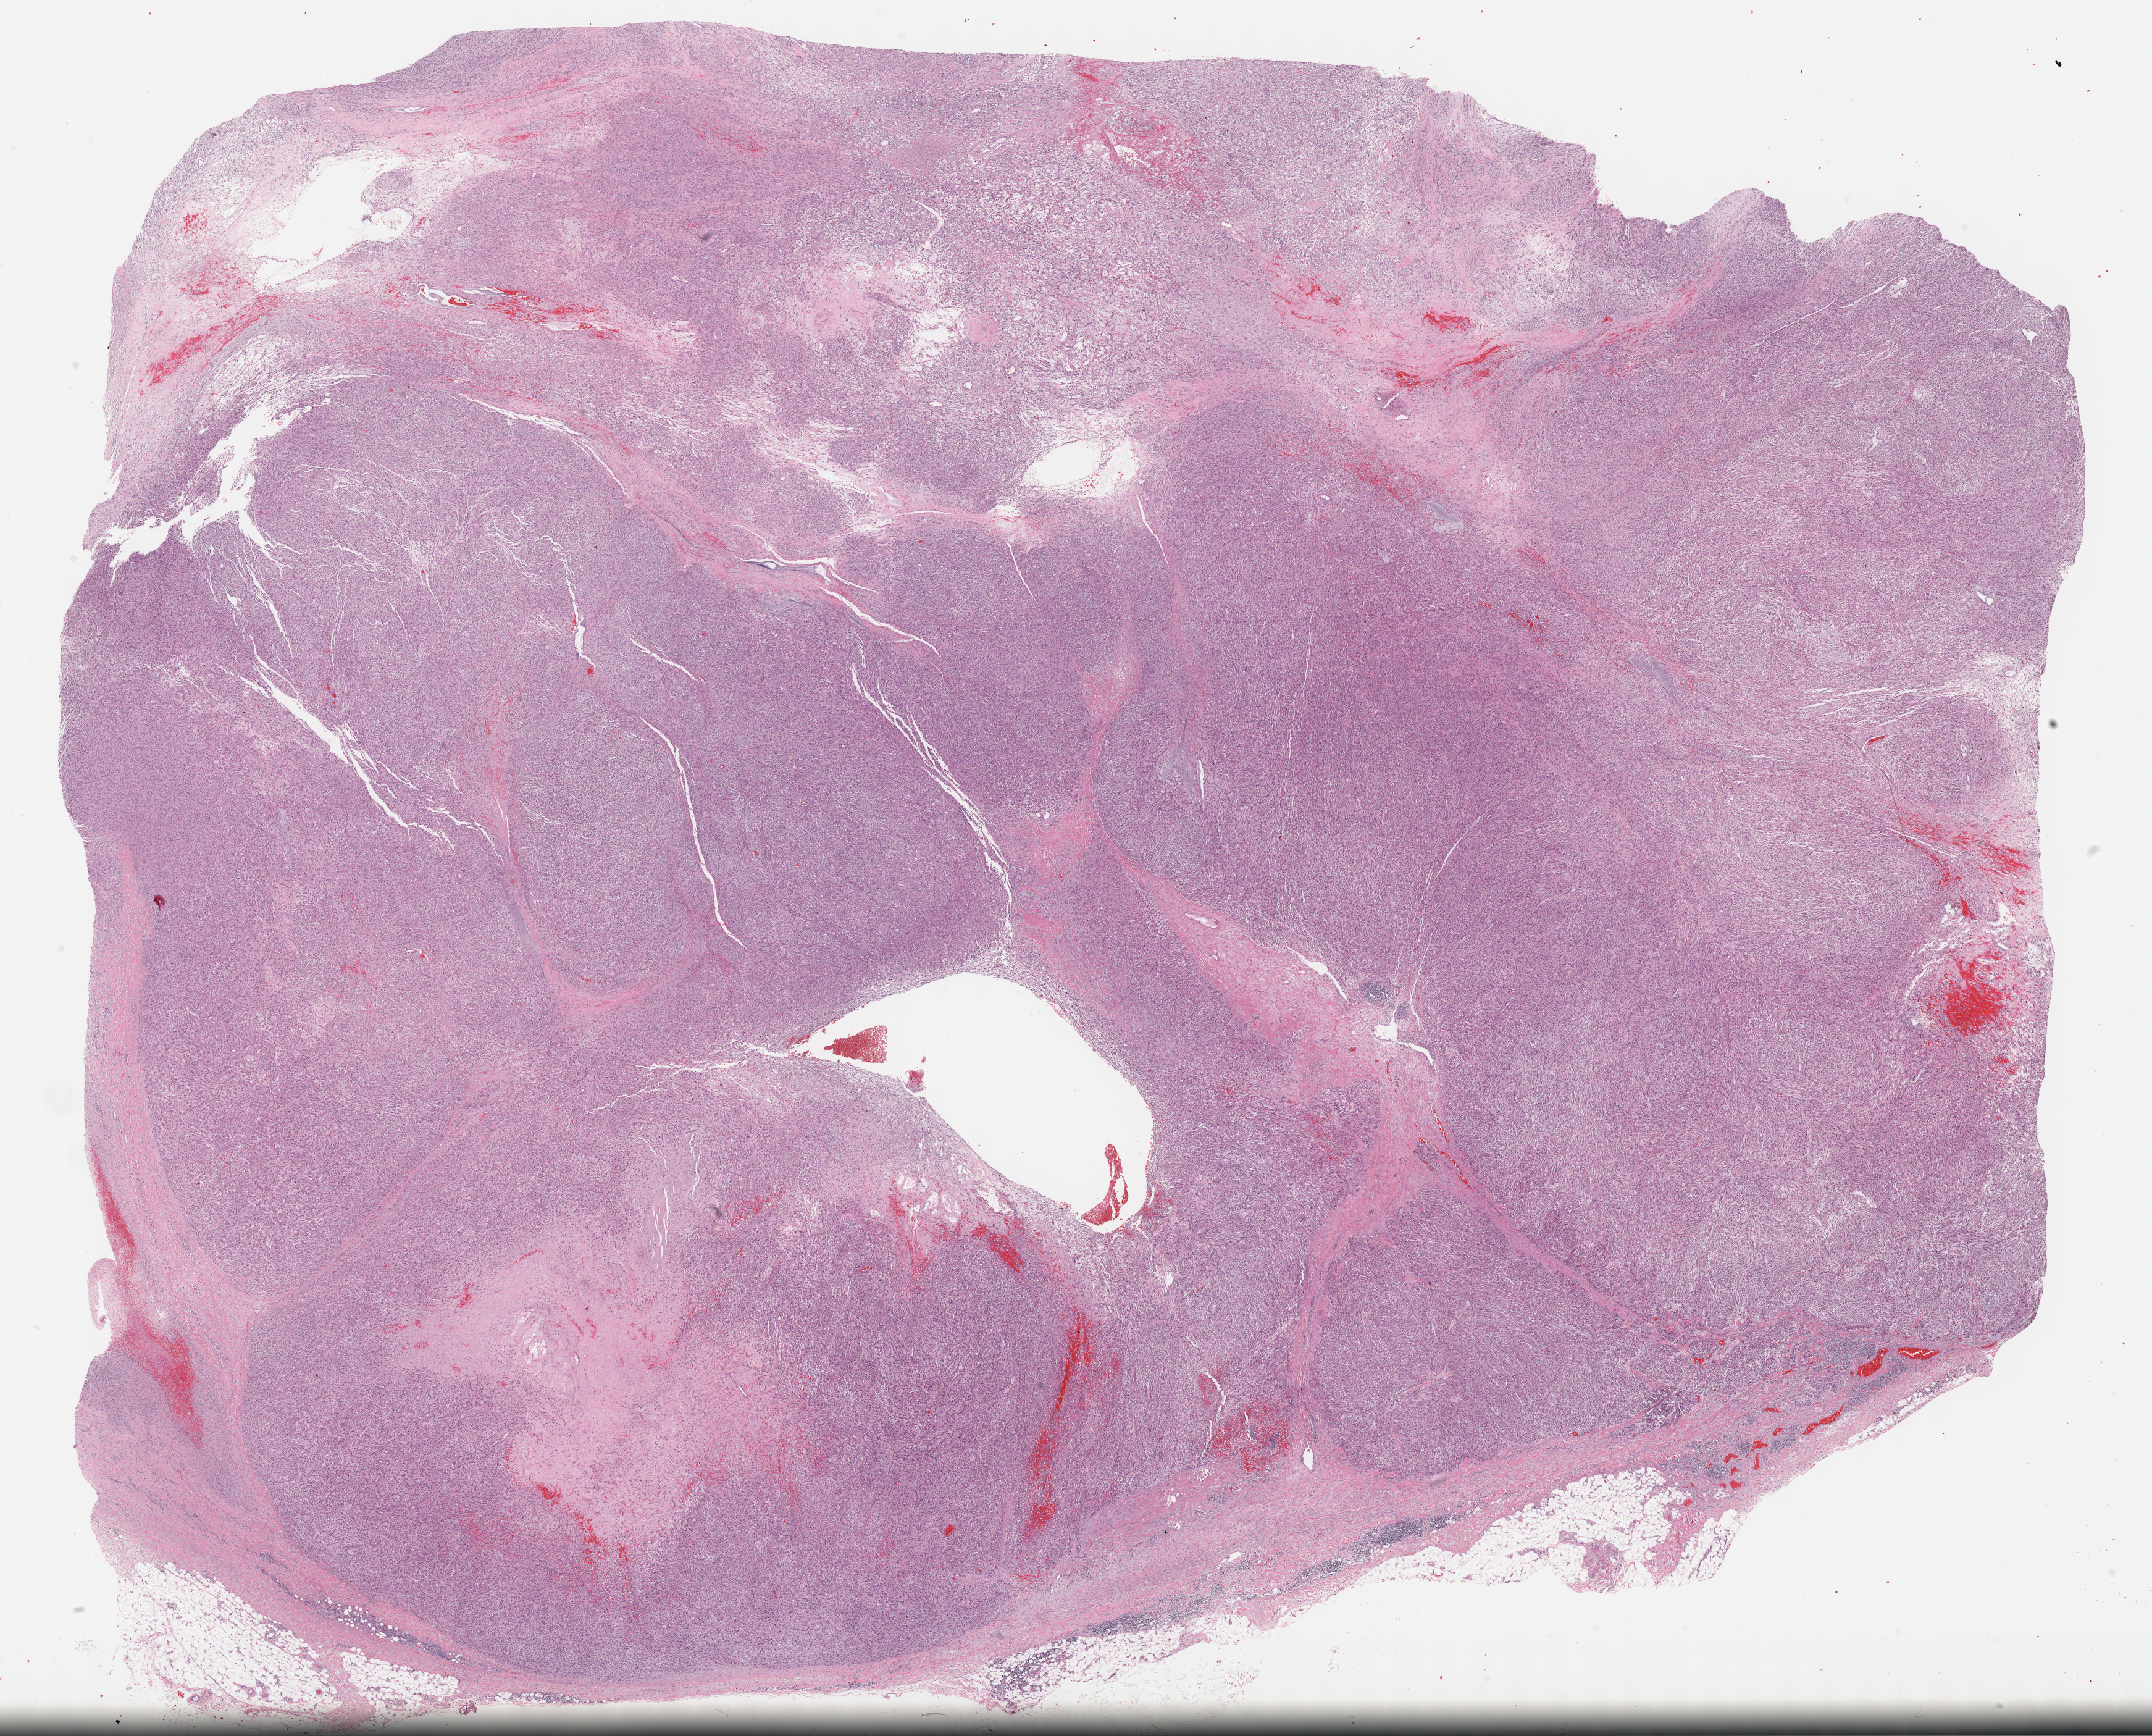
H&E-stained whole-slide image, low-resolution overview of the scanned area, about 28.2 x 22.7 mm (from a 40x scan), formalin-fixed paraffin-embedded (FFPE) diagnostic section, primary tumour sample from the connective, subcutaneous and other soft tissues. Patient: male, age at initial diagnosis 67 years.
Diagnosis: Leiomyosarcoma, NOS (connective, subcutaneous and other soft tissues of lower limb and hip).